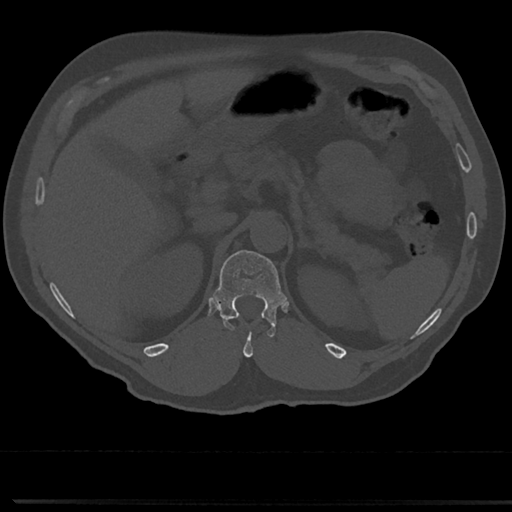
CT including the spine, one axial slice. 120 kVp. Bone window (W 1800 / L 400 HU). 512 × 512 image matrix. Patient: male, 61 years. Case-level facts recorded for this patient, not image findings: primary cancer: prostate.
Outlined on this slice (semi-automatically segmented with operator editing):
- T12 vertebra: bounding box (x1, y1, x2, y2) in pixels: (217, 249, 282, 334)